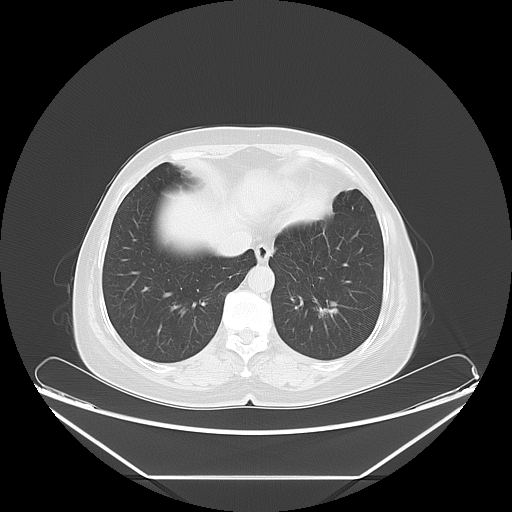
Chest CT, one axial slice. Reconstruction kernel LUNG. 120 kVp. Lung window (W 1500 / L -600 HU). 512 × 512 image matrix. Patient: female, 63 years. From the clinical record (not read from this slice): clinical TNM (as recorded): T1c N0 M0; histopathological grade: G2-3.
Outlined on this slice (rectangle marked by the reading radiologist):
- lung tumour (recorded histology: adenocarcinoma): bounding box [x1, y1, x2, y2] px = [310, 297, 341, 327]